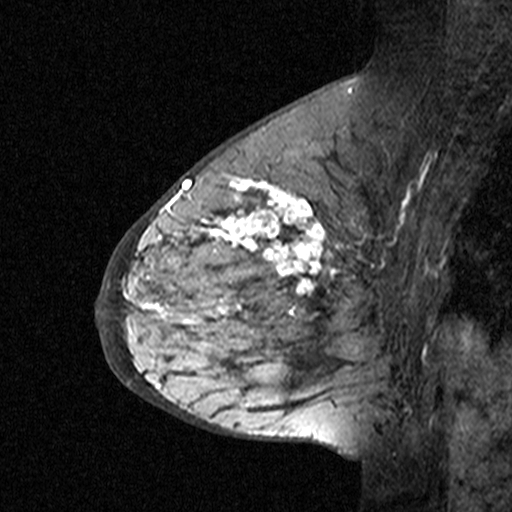
Breast MRI (dynamic contrast-enhanced), one sagittal slice. Position 21 of 44 along the scan axis. Dynamic contrast-enhanced study with each time point stored as its own series, time point 3 of 4 at this slice position (ordered by acquisition time). 1.5 T. TE 4.5 ms, TR 11 ms. 3 mm slice thickness. 512 × 512 image matrix, field of view 200 × 200 mm. Female patient, age 65 years. Case-level facts recorded for this patient, not image findings: setting: breast cancer imaged before/during neoadjuvant chemotherapy; receptor status: HER2-positive.
Outlined on this slice (semi-automatically segmented with operator editing):
- analysis volume of interest (the breast-tissue region the enhancement analysis was run in; not a lesion): box from (x=182, y=190) to (x=353, y=361) px
- tumour enhancement mask (voxels above the 90 % enhancement threshold inside the analysis volume of interest): (x=182, y=190)–(x=331, y=315)